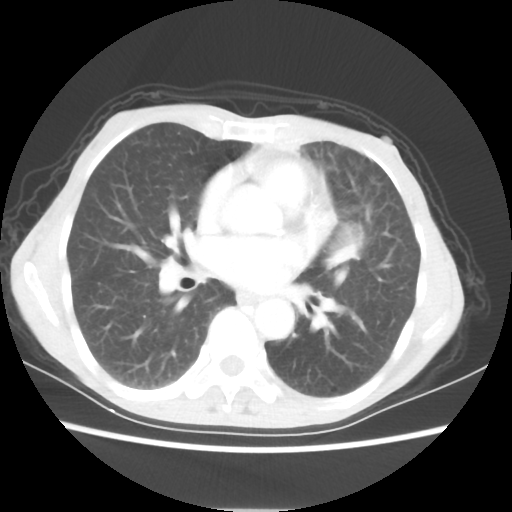
Chest CT, one axial slice. Slice 30 of 56 in the series (ordered by position). Reconstruction kernel STANDARD. 80 kVp. Lung window (W 1500 / L -600 HU). 5 mm slice thickness. 512 × 512 image matrix. Patient: female, 60 years. Case-level facts recorded for this patient, not image findings: clinical TNM (as recorded): T4 N1 M0.
Outlined on this slice (bounding box drawn by a radiologist):
- lung tumour (recorded histology: adenocarcinoma): bounding box [x1, y1, x2, y2] px = [325, 242, 368, 271]